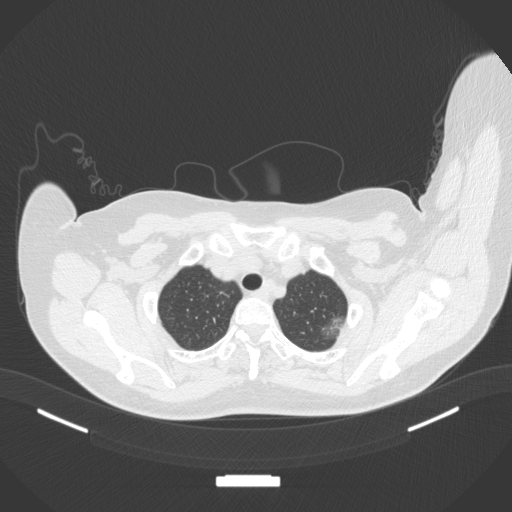
Chest CT, one axial slice. Lung window (W 1500 / L -600 HU). 1 mm slice thickness. 512 × 512 image matrix. Female patient, age 58 years. Case-level facts recorded for this patient, not image findings: clinical TNM (as recorded): T1c N0 M0.
Outlined on this slice (bounding box drawn by a radiologist):
- lung tumour (recorded histology: adenocarcinoma): bounding box (x1, y1, x2, y2) in pixels: (316, 316, 348, 348)